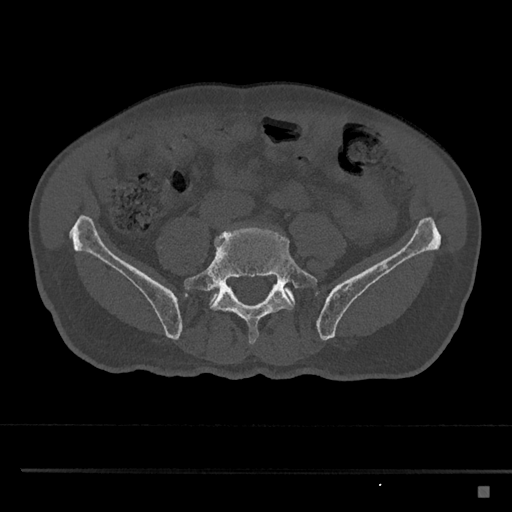
CT including the spine, one axial slice; position 580 of 797 along the scan axis; reconstruction kernel Br40s/3; bone window (W 1800 / L 400 HU); 512 × 512 image matrix. Patient: male, 59 years. From the clinical record (not read from this slice): primary cancer: prostate.
Annotated regions visible in this slice (semi-automatic segmentation, software-assisted and operator-edited):
- L5 vertebra: bounding box <183,227,318,345> (left, top, right, bottom; pixels)